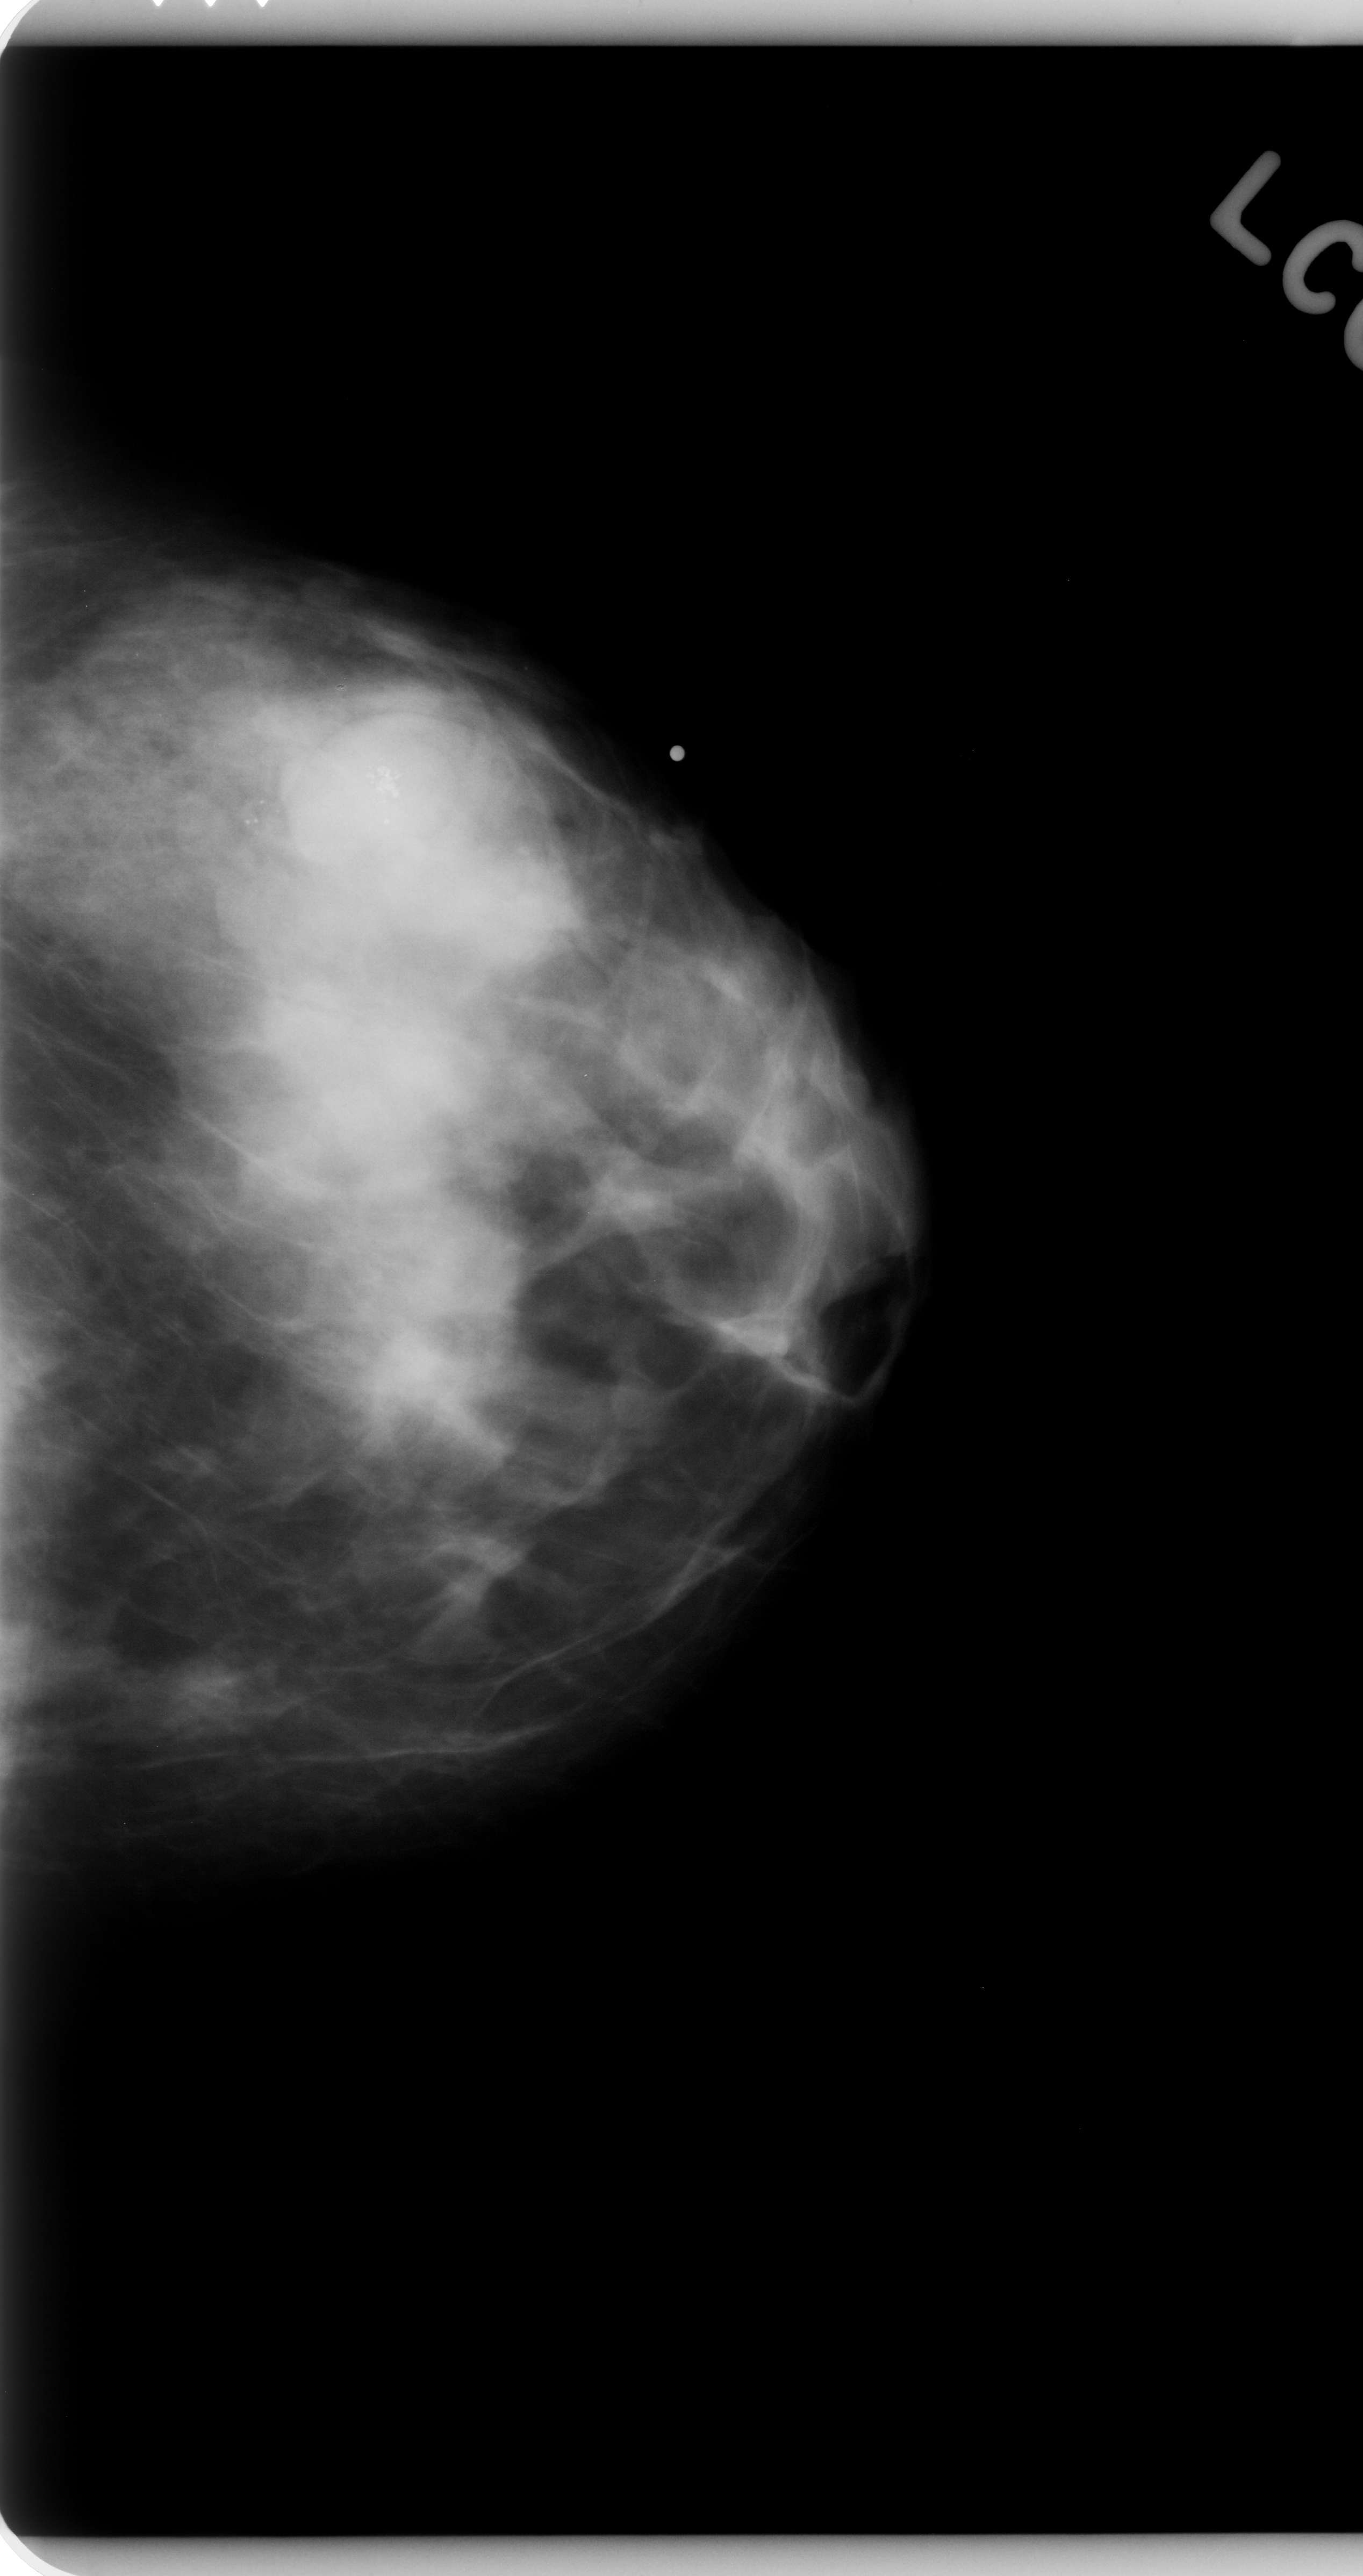
Scanned film-screen mammogram. Left breast. Craniocaudal (CC) view. Breast composition: heterogeneously dense (BI-RADS density category 3 of 4). 1363 × 2576 image matrix.
Expert-marked regions of interest on this film, with their recorded descriptors:
- mass, shape lobulated, margins obscured; BI-RADS assessment category 3; subtlety rating 3 on a 1 (subtle) to 5 (obvious) scale; pathology result (as recorded, not read from the image): benign: bounding box [x1, y1, x2, y2] px = [281, 667, 483, 868]